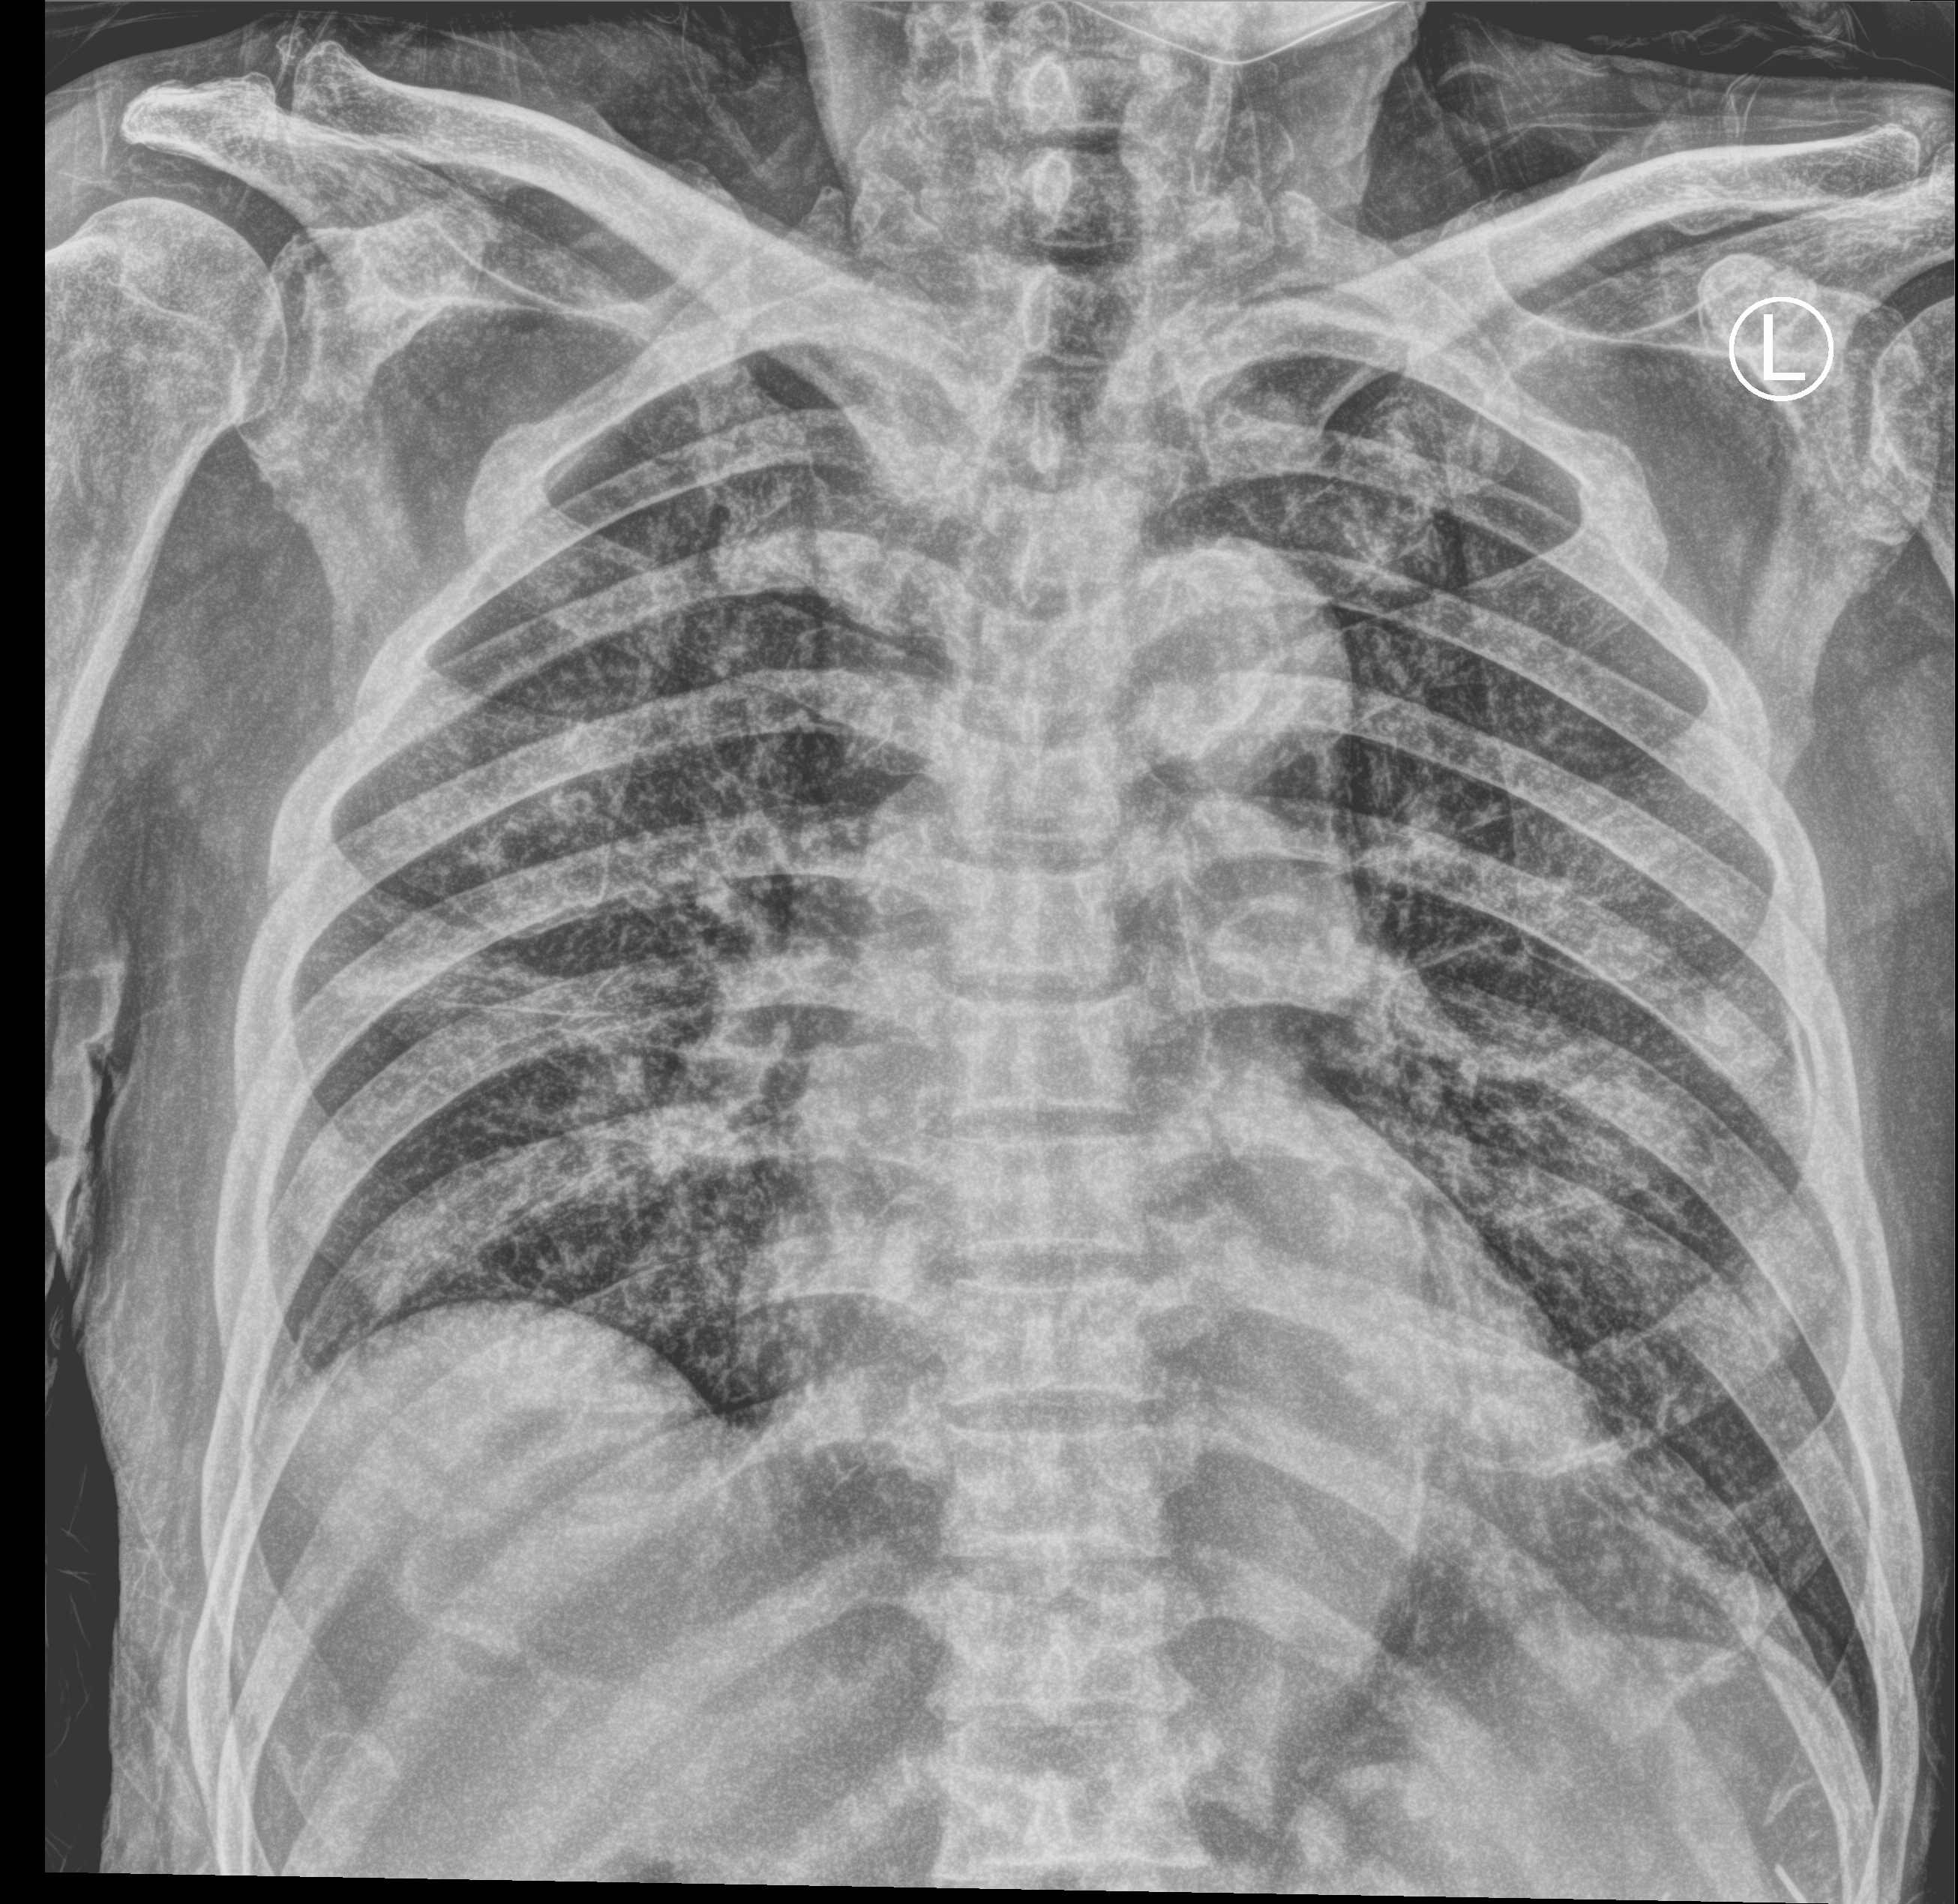
Portable chest radiograph. Patient hospitalised with COVID-19; male, aged 75–90 years.
From the hospital-stay record, not from the radiograph (when in the stay this image was taken is not recorded): length of hospital stay: 12 days; mechanically ventilated during this hospital stay: no; admitted to intensive care during this hospital stay: no.